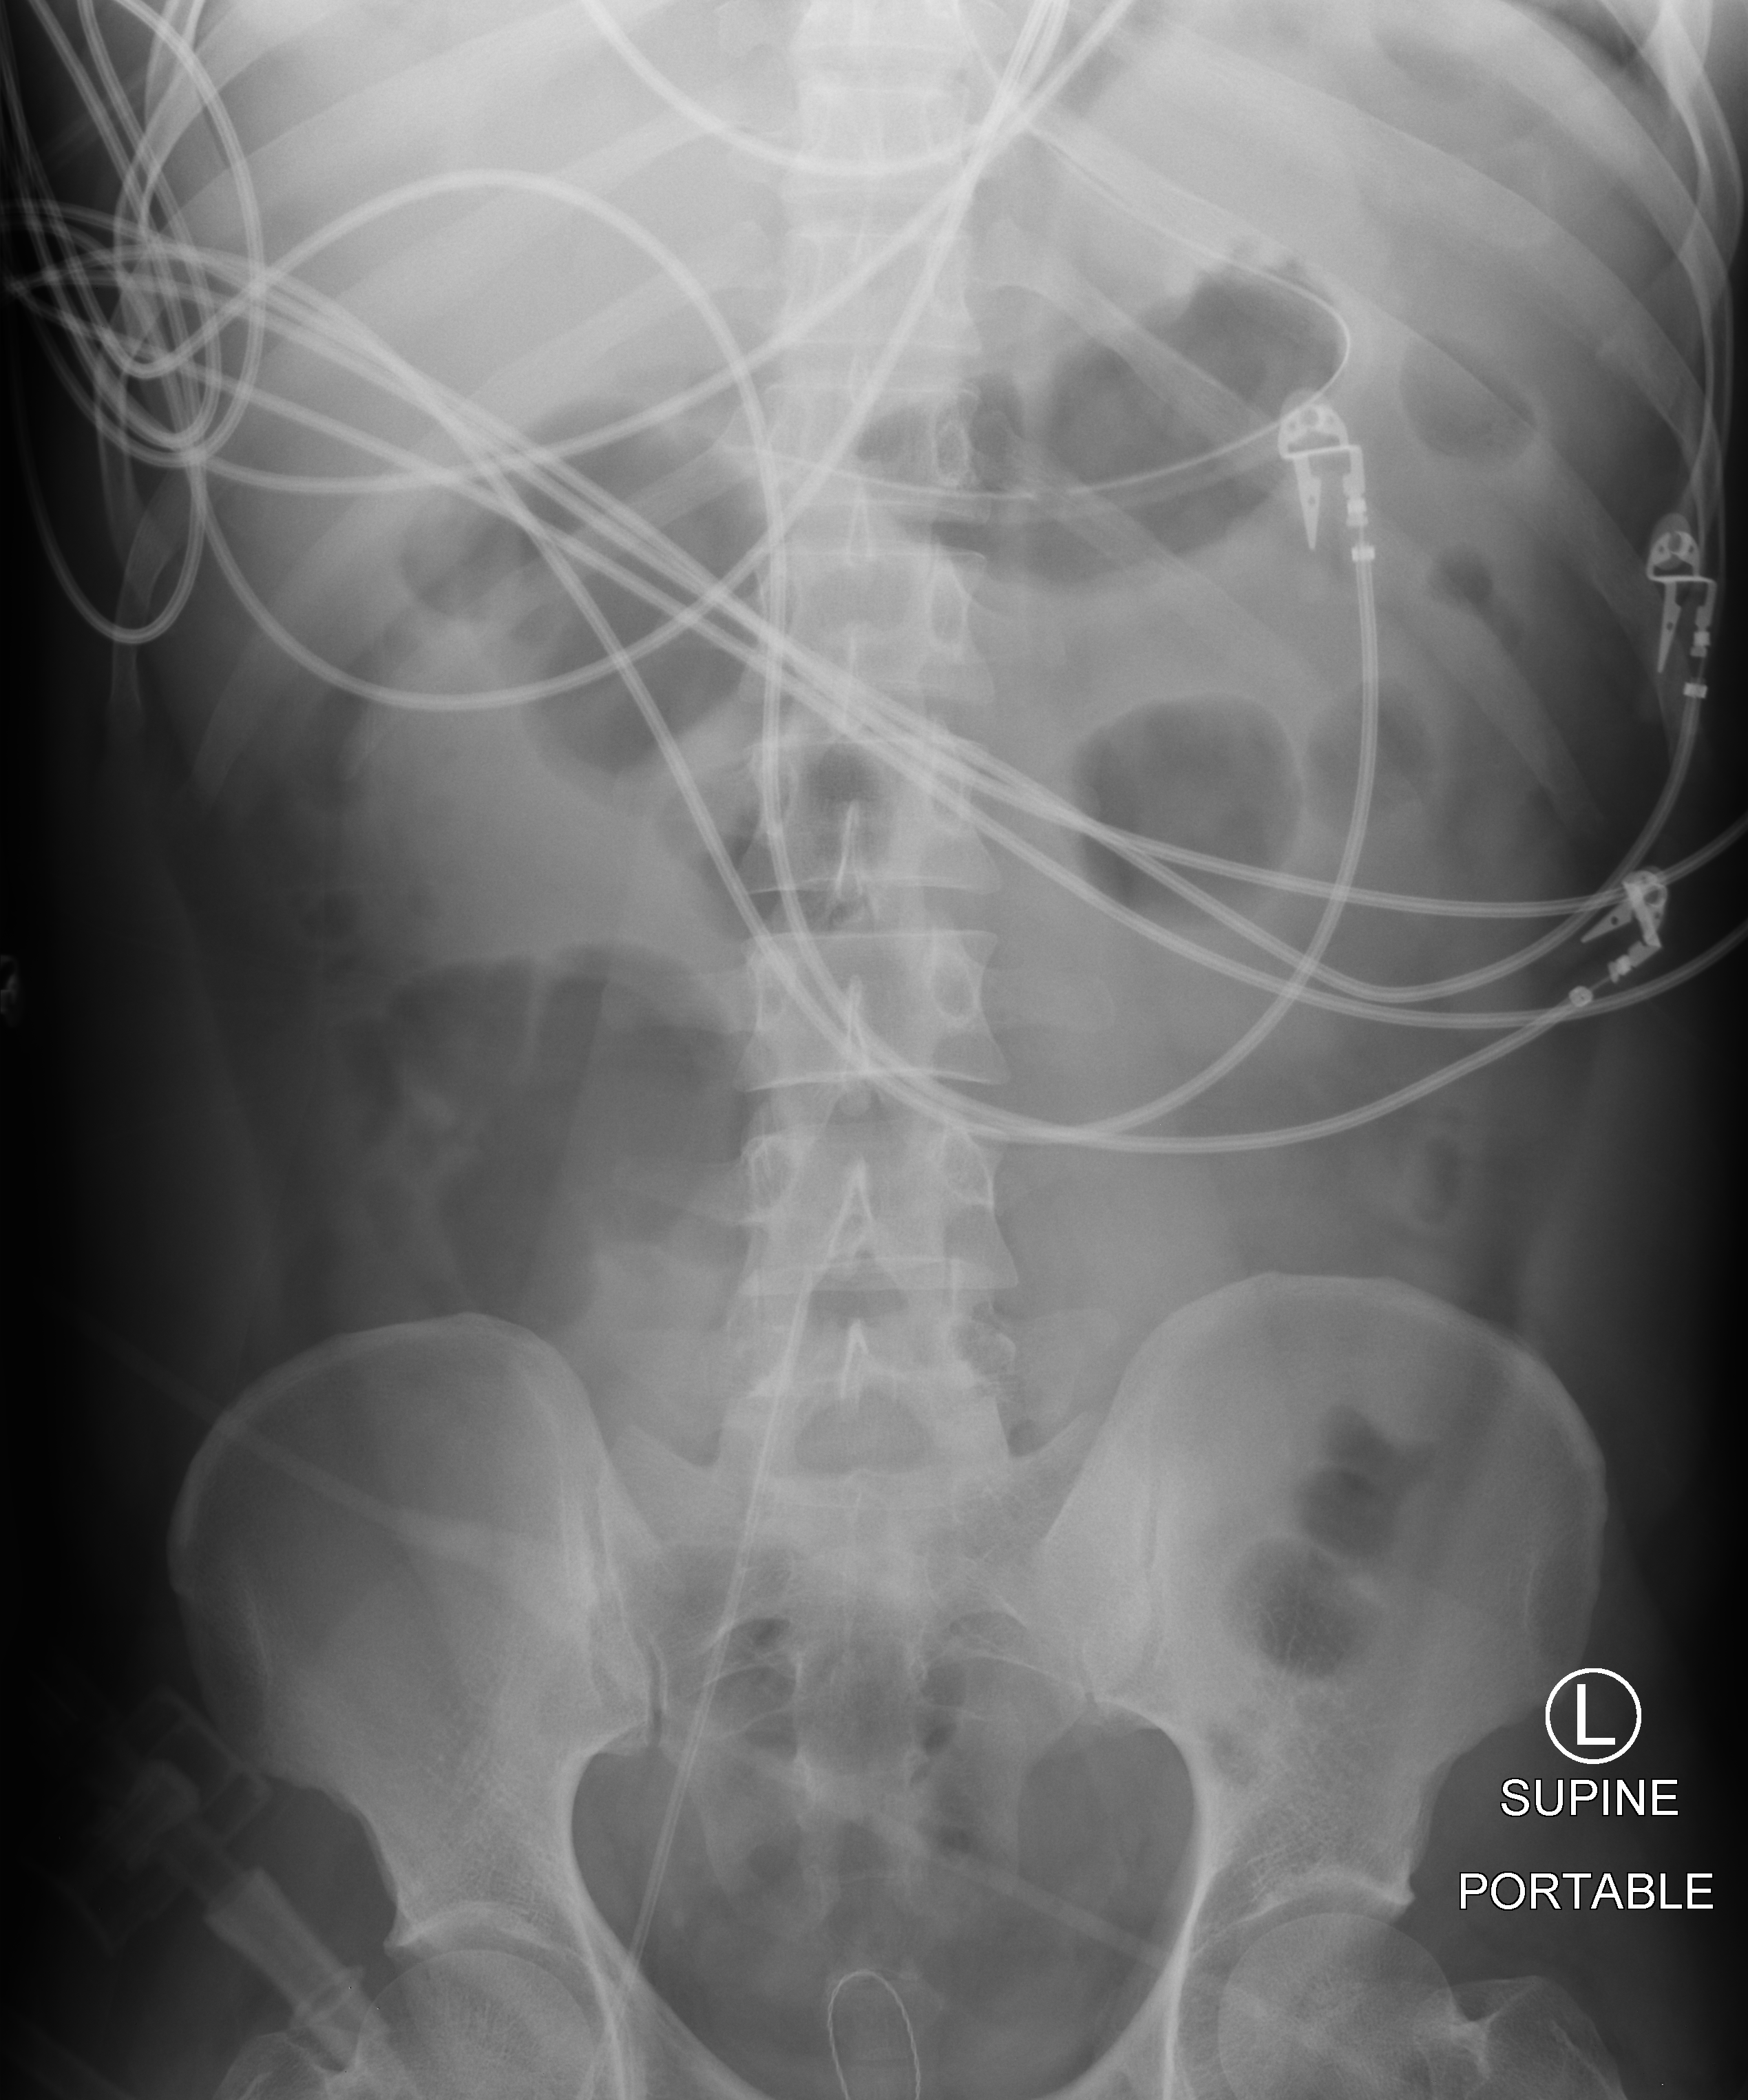
Abdomen X-ray (portable), anteroposterior (AP) projection. Male patient hospitalised with COVID-19, age 18–59 years.
Hospital-stay facts (about this admission, not read from this image; timing relative to this image not recorded): admitted to intensive care during this hospital stay: yes; length of hospital stay: 31 days; mechanically ventilated during this hospital stay: yes.